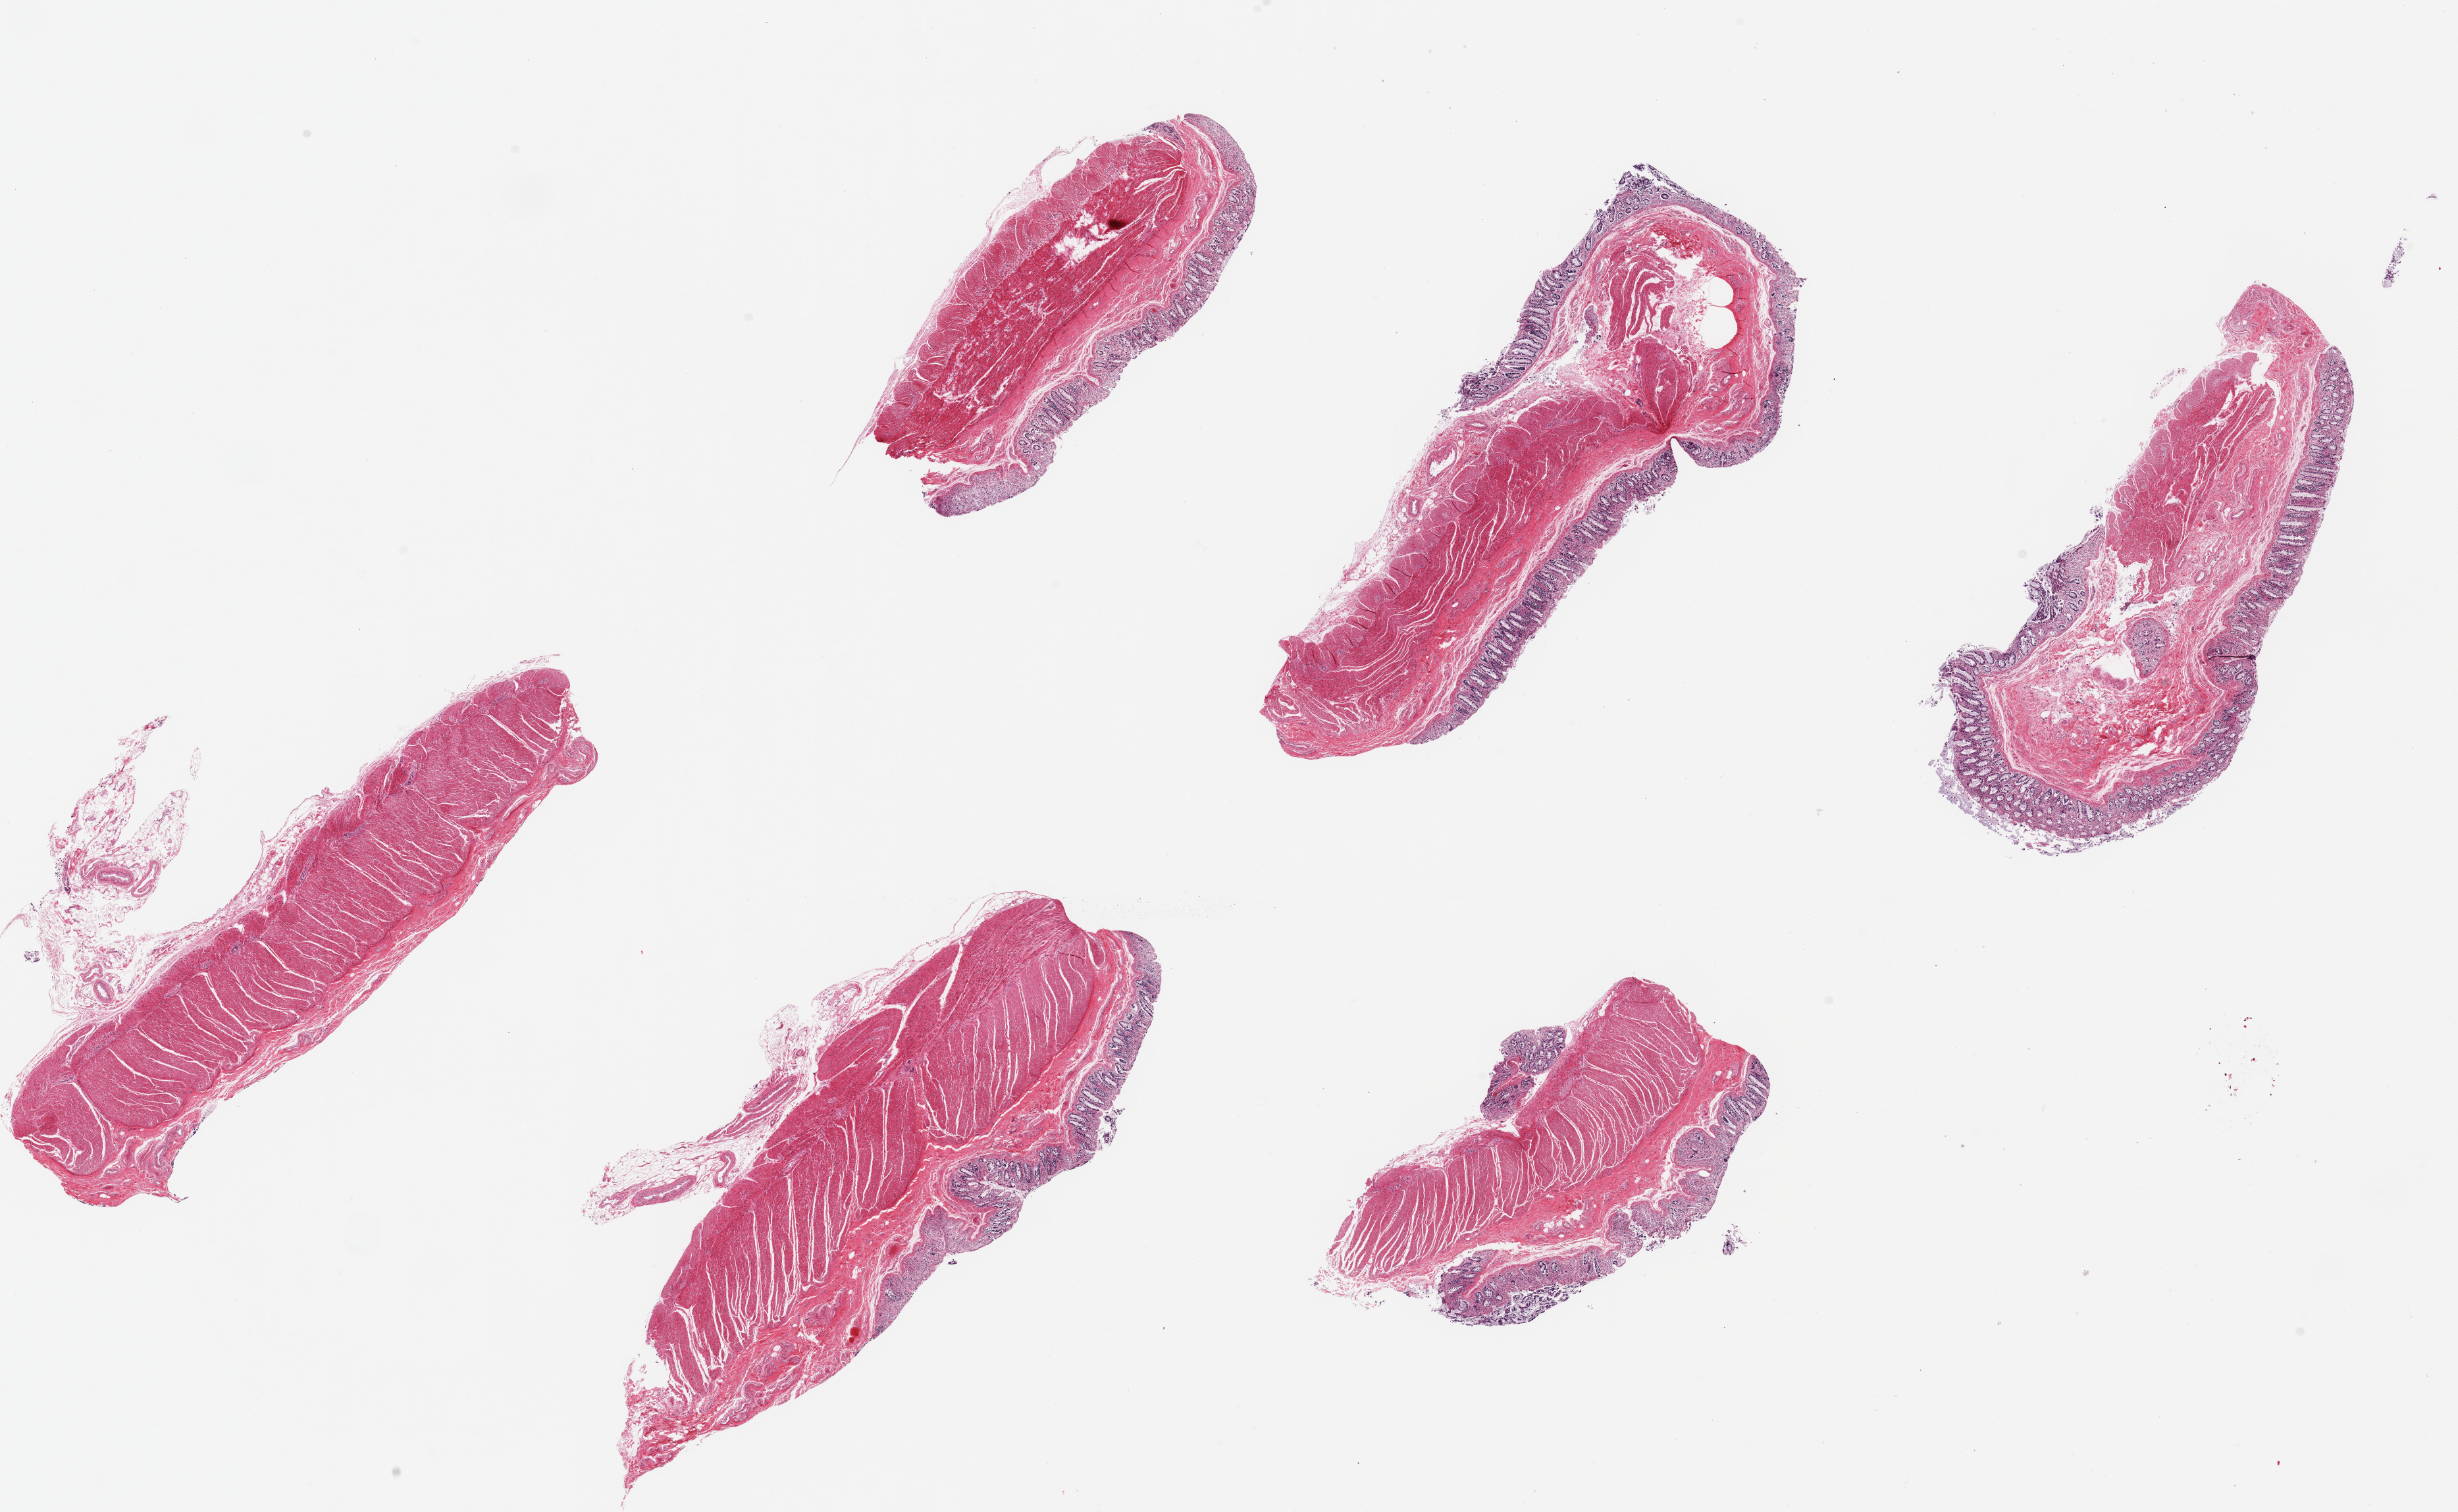
Digitized H&E-stained section, brightfield, shown as a low-resolution overview of the whole scanned area (about 29.5 x 18.2 mm). PAXgene-fixed, paraffin-embedded tissue. Section of transverse colon (target tissue). Tissue donor sample. Female donor.
Pathologist's review note for this sample: 6 pieces, up to 9x5mm; mucosa=3; muscularis =2.